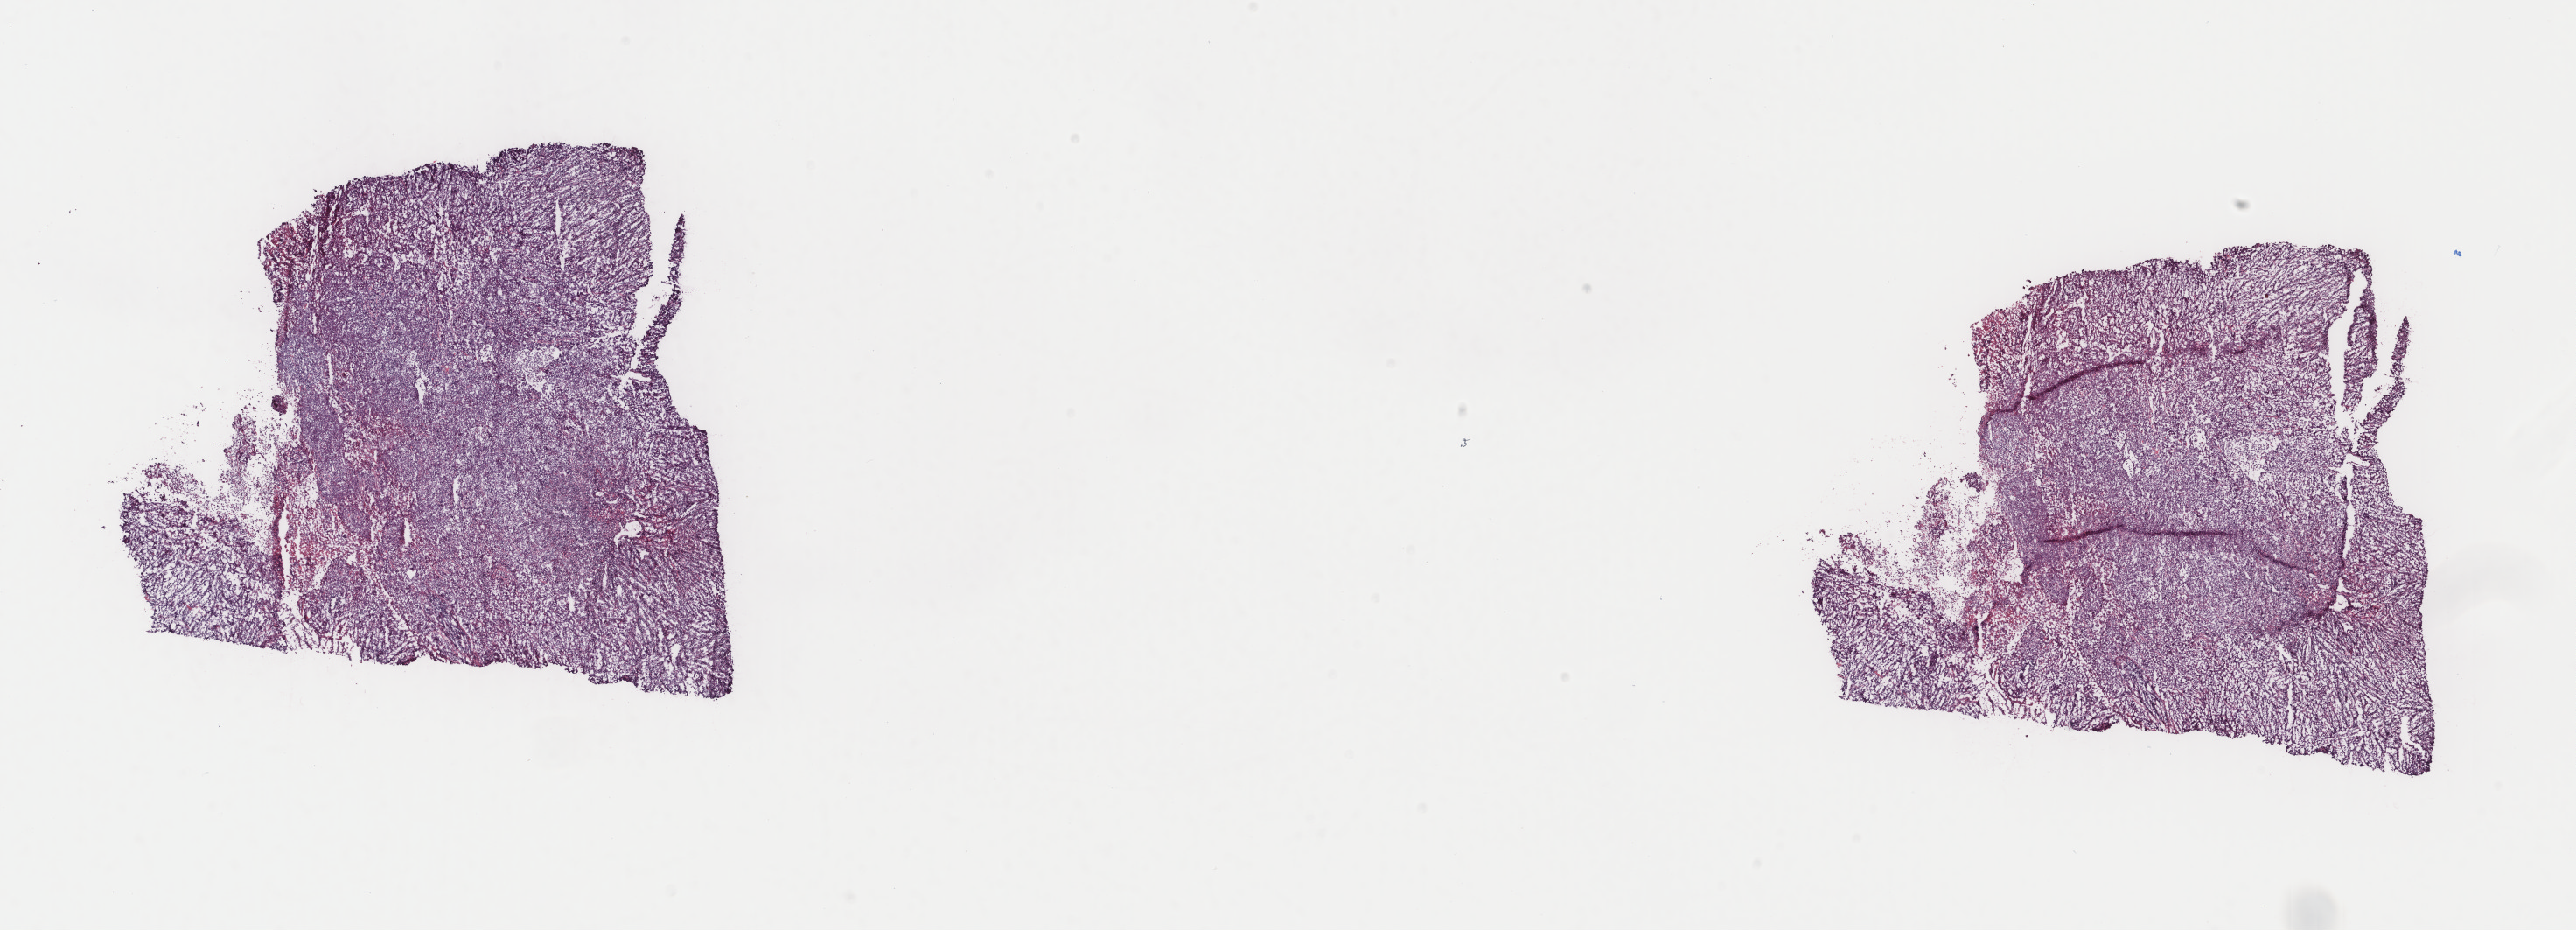
Whole-slide histology image, H&E, low-resolution overview of the scanned area, about 23.4 x 8.4 mm (slide scanned at 40x). Frozen section from the top of the tissue portion. Sample: primary tumour, bladder. Male, age 57 years at initial diagnosis. Histologic grade: high grade. Pathologist review of this section (percent, as recorded): tumour cells 80%, tumour nuclei 60%, normal cells 0%, stromal cells 15%, necrosis 5%. Infiltration values recorded for this section: lymphocyte infiltration 15%, monocyte infiltration 2%, neutrophil infiltration 8%.
Diagnosis: Transitional cell carcinoma. Lymph nodes positive (case pathology): 0 of 47 examined. AJCC pathologic stage: III (7th edition). TNM: T3 N0 M0.